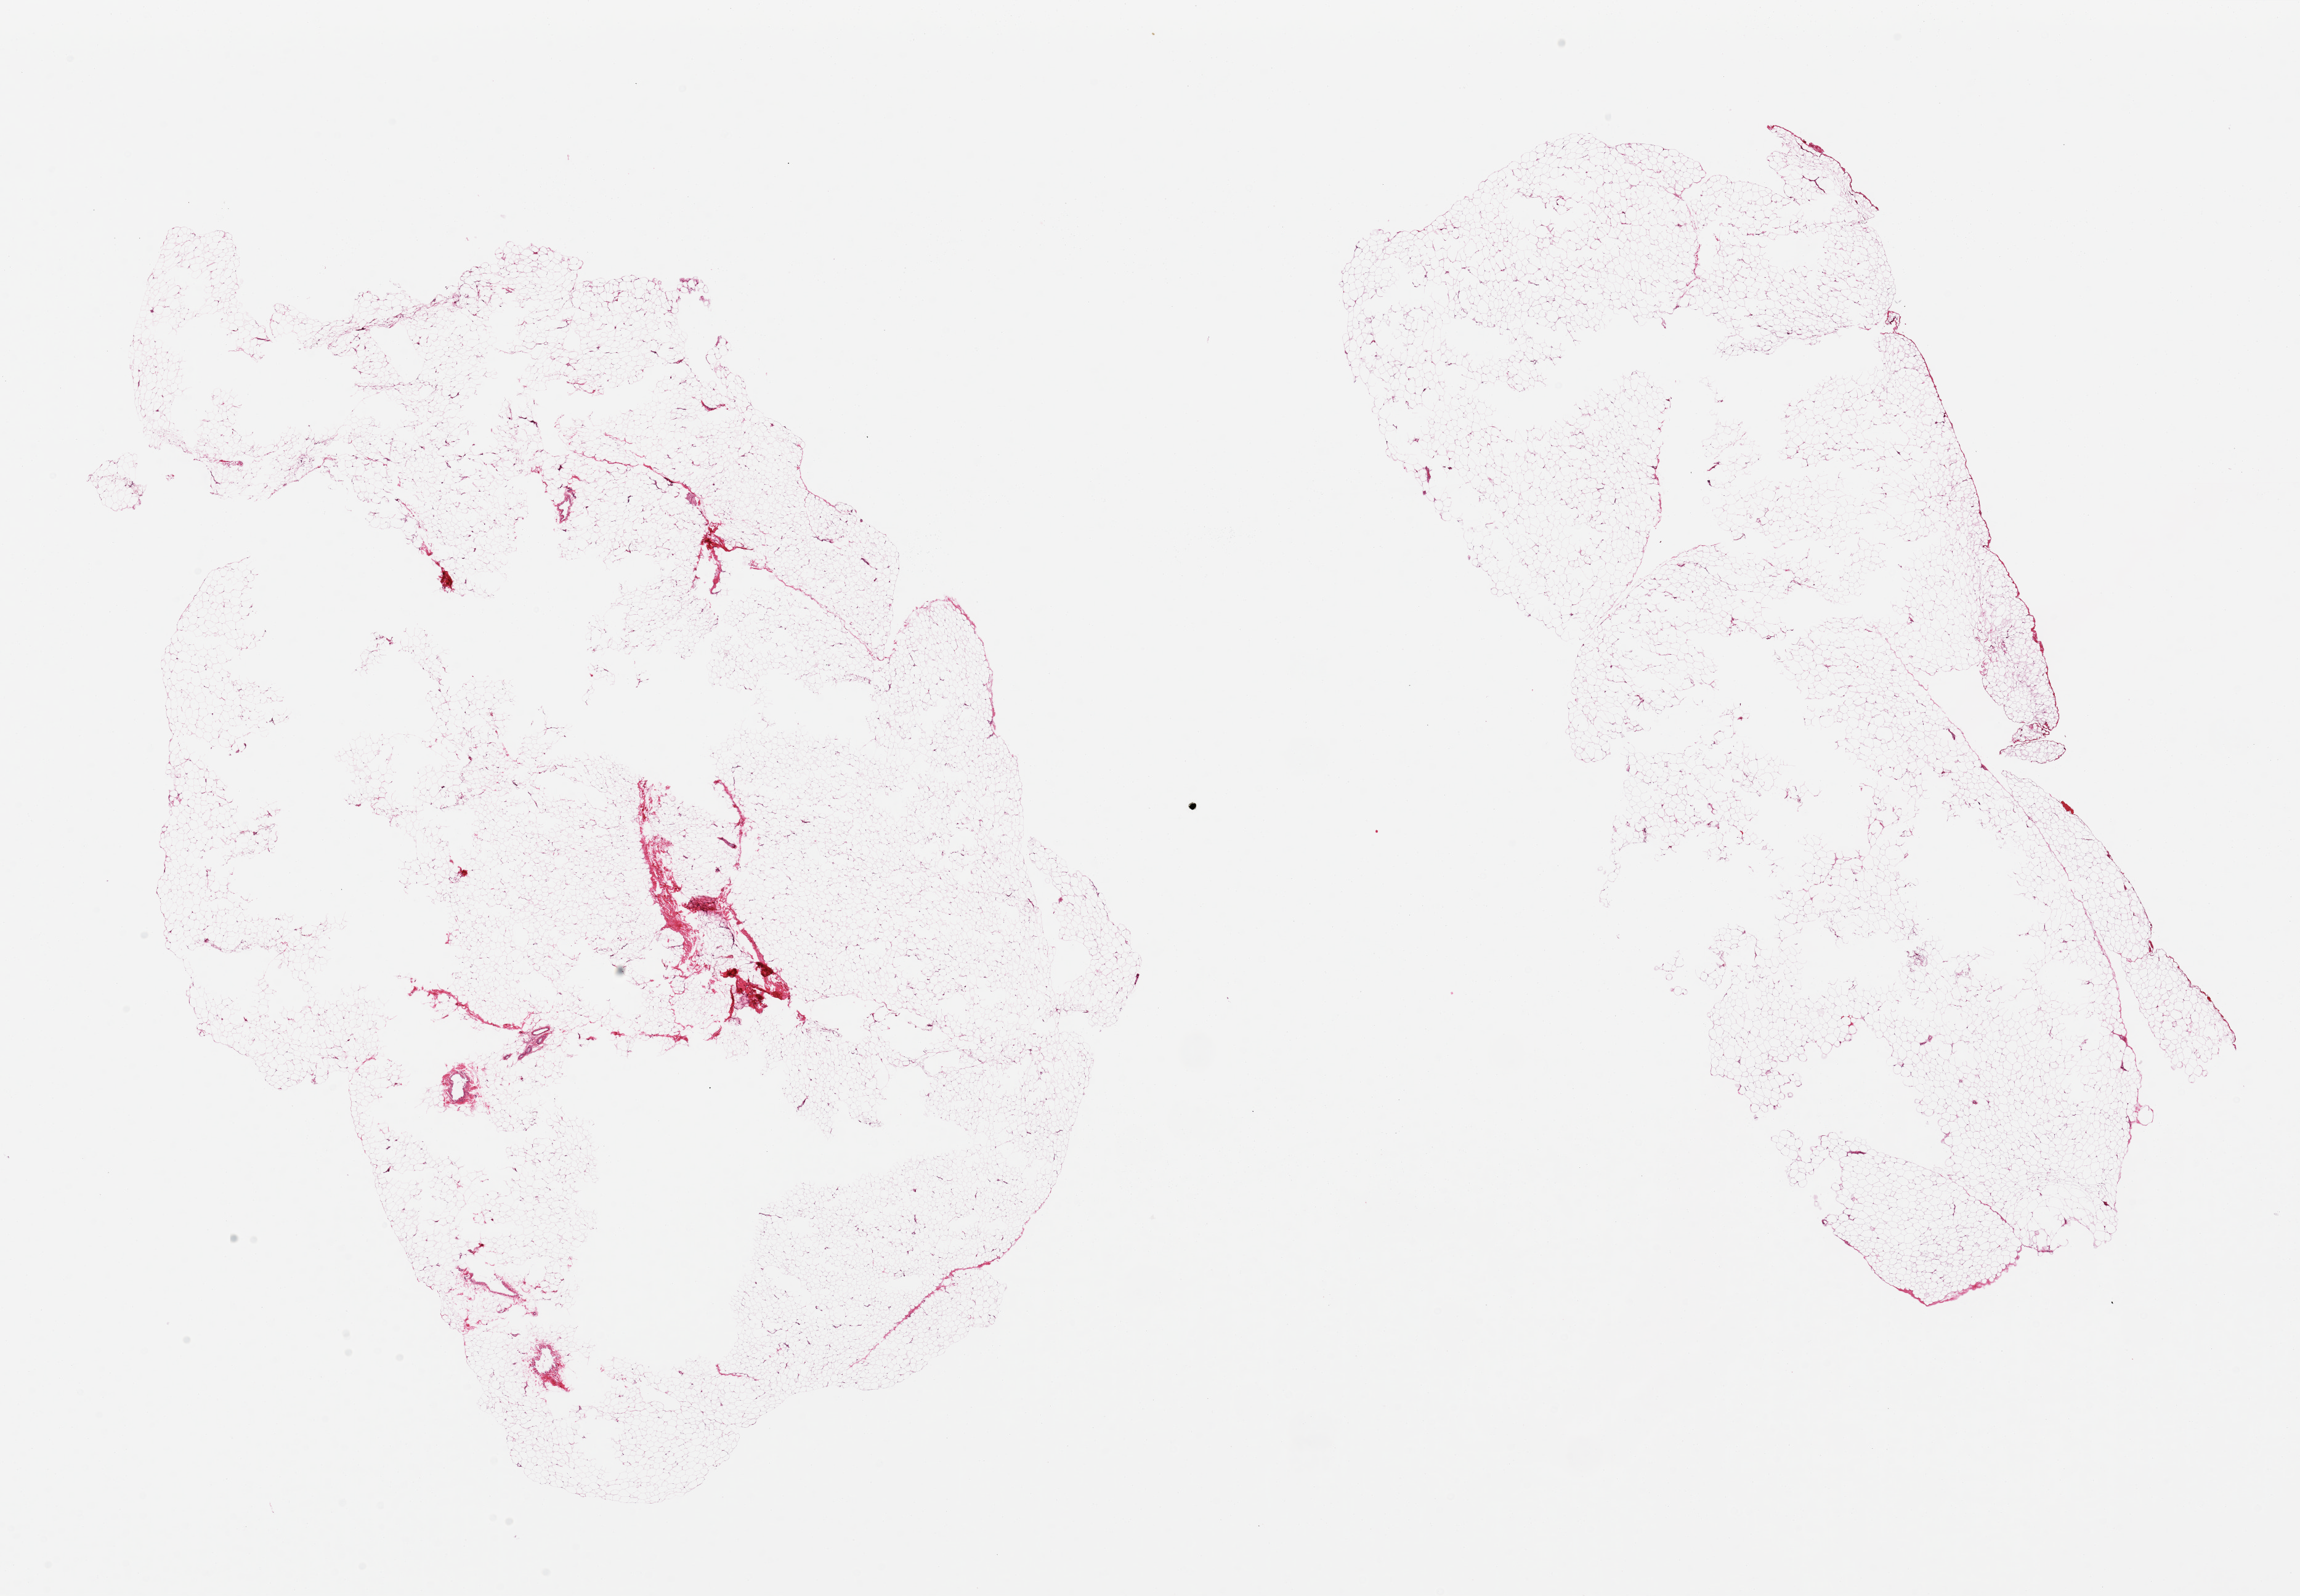
Hematoxylin and eosin (H&E) whole-slide image, a low-resolution overview of the entire scanned area, about 29.5 x 20.5 mm (slide scanned at 20x), PAXgene-fixed, paraffin-embedded tissue, target tissue: adipose tissue, tissue donor sample. Donor: male.
* pathologist's review note for this sample: 2 pieces, trace fascia